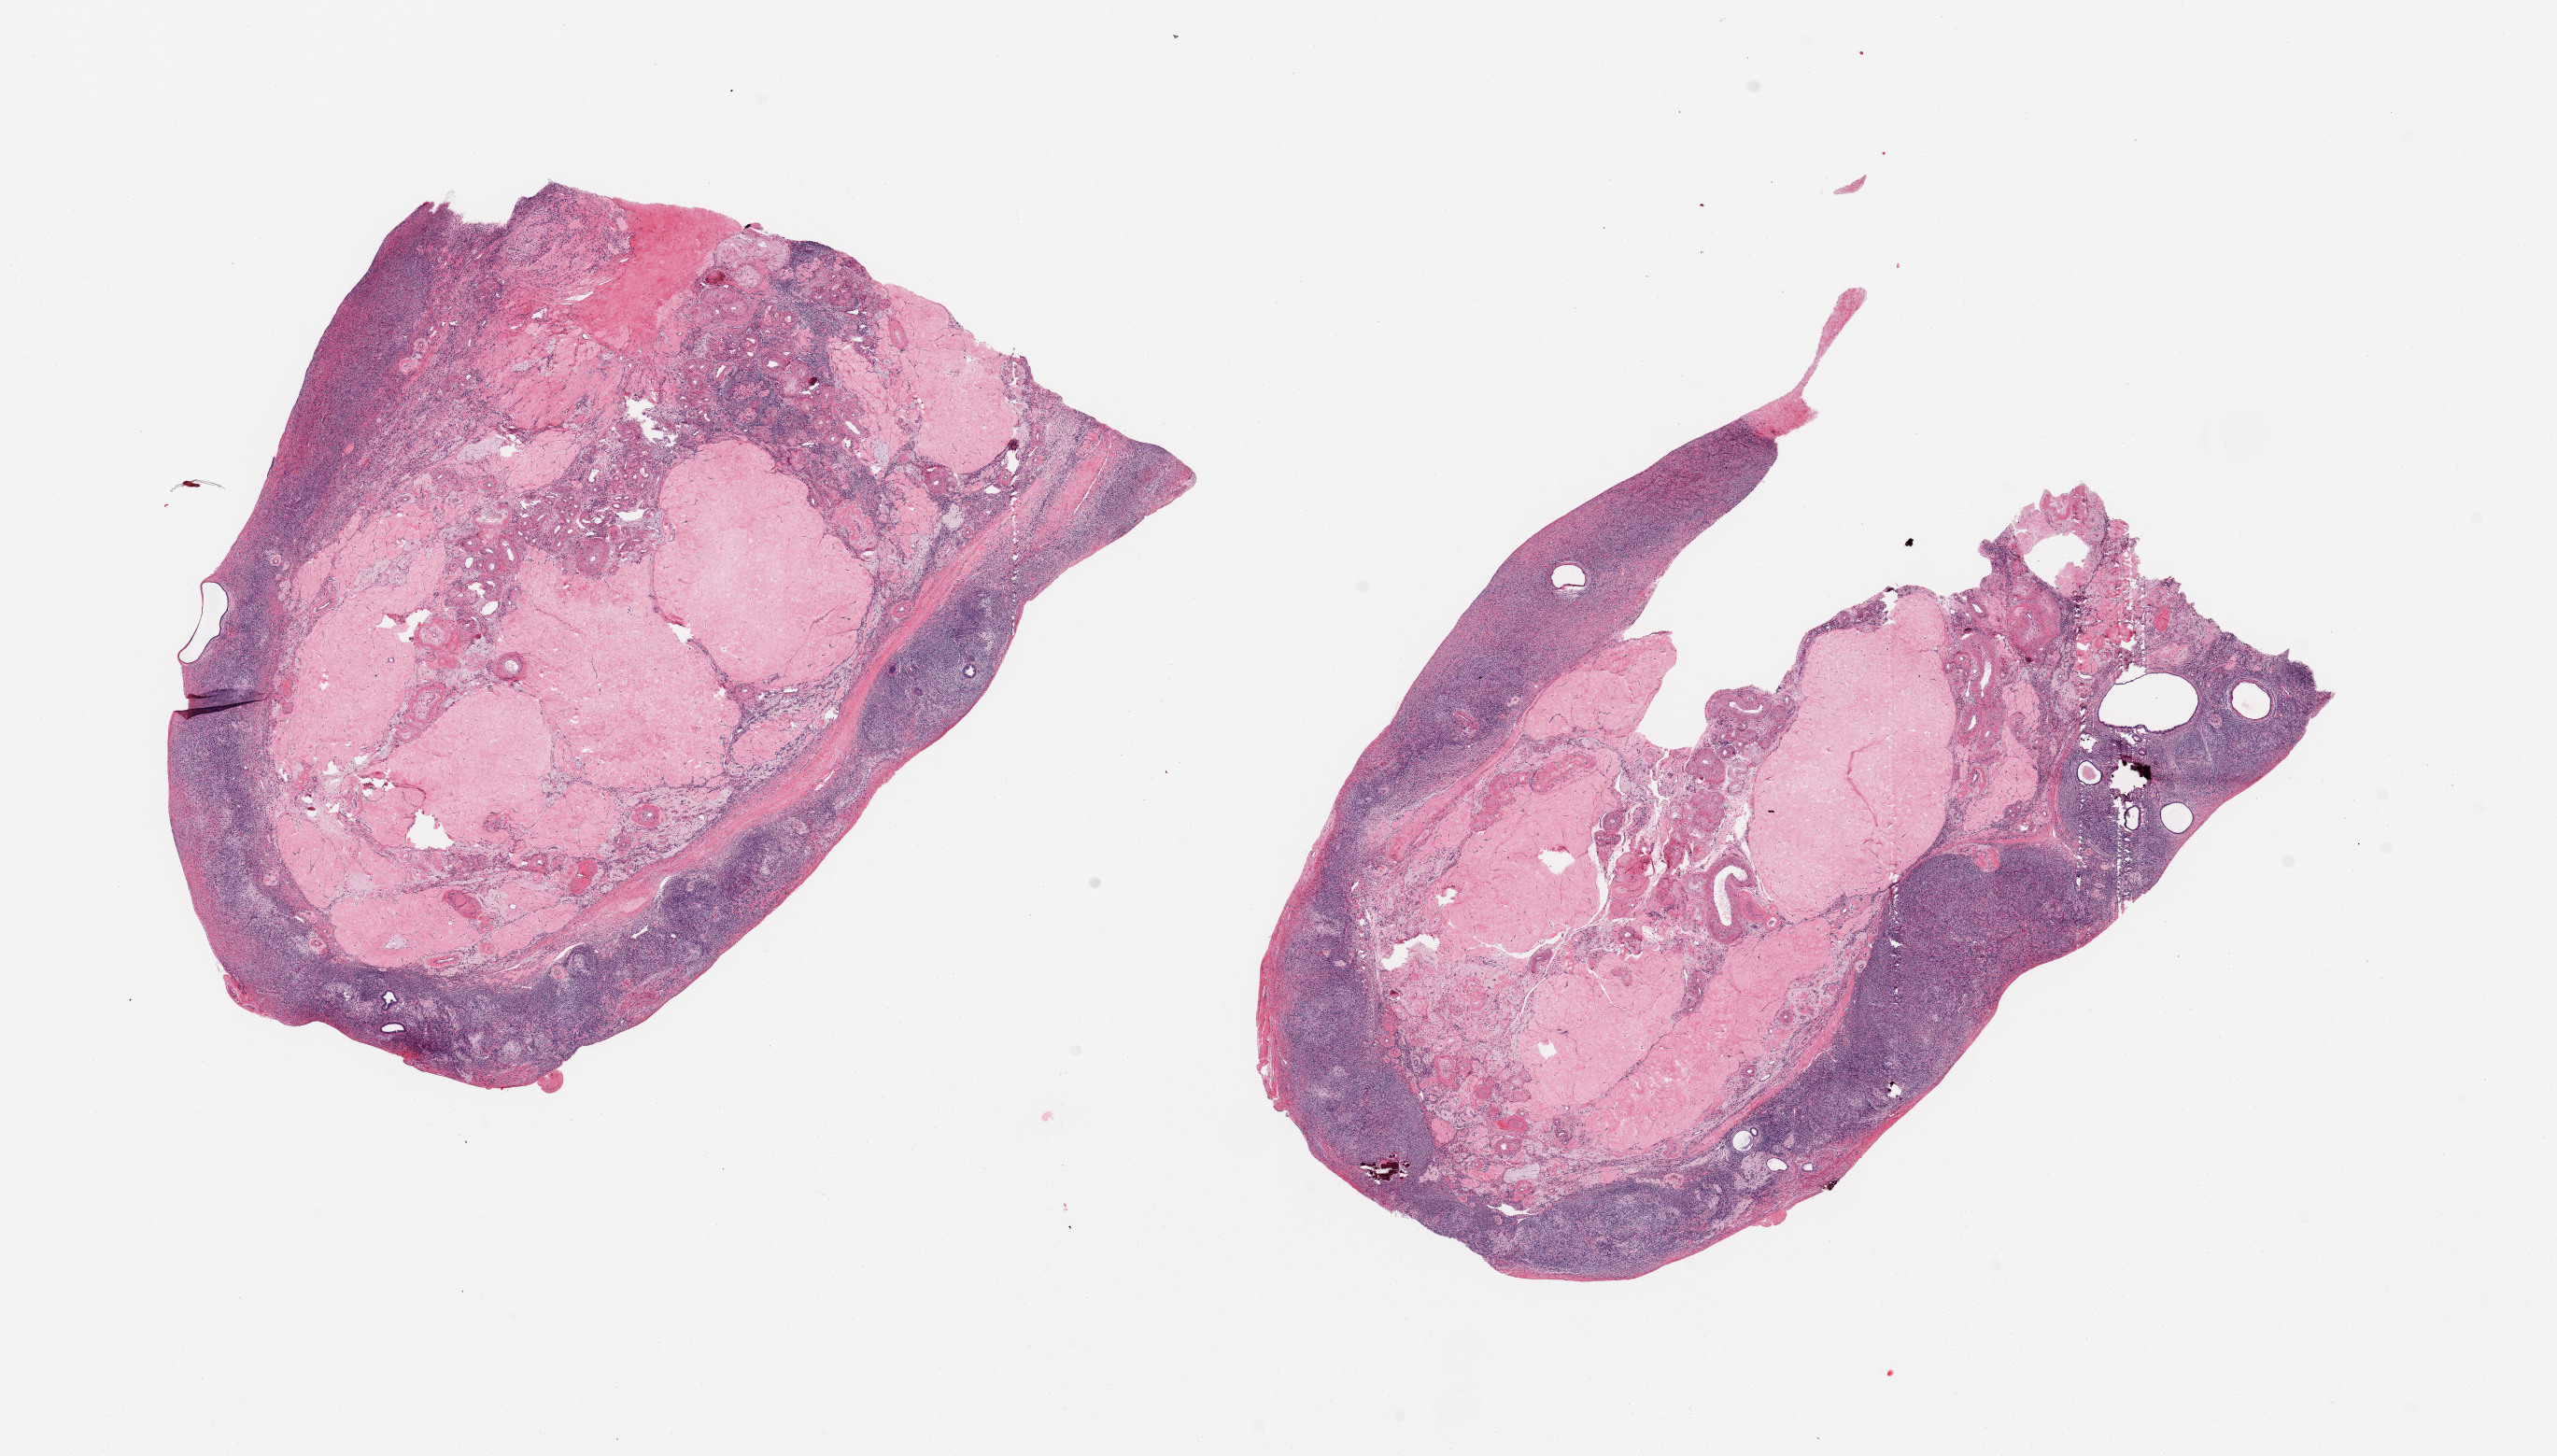
Whole-slide image, H&E stain, low-resolution overview of the scanned area, about 21.7 x 12.3 mm (acquisition: 20x scan); PAXgene-fixed, paraffin-embedded tissue; target tissue: ovary; donor tissue sample. Donor: female.
Review note (as recorded): 2 pieces; large corpora albicantia, few inclusion glands, focal calcifications.